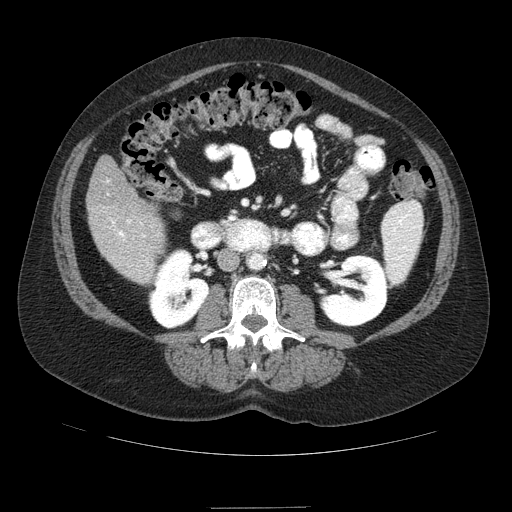
Contrast-enhanced abdominal CT (liver protocol), one axial slice; position 23 of 89 along the scan axis; reconstruction kernel STANDARD; 120 kVp; soft-tissue window (W 400 / L 40 HU); 2.5 mm slice thickness; 512 × 512 image matrix, field of view 400 × 400 mm. Case-level facts recorded for this patient, not image findings: diagnosis: hepatocellular carcinoma (patient treated with transarterial chemoembolisation; whether this scan precedes or follows treatment is not stated here); TNM stage (as recorded): Stage-IIIB; Child-Pugh class: A; tumour nodularity: multinodular.
Outlined on this slice (semi-automatic segmentation, software-assisted and operator-edited):
- liver parenchyma outside the tumour (the mass and vessels are separate outlines, so this box may not span the whole liver): bounding box (x1, y1, x2, y2) in pixels: (87, 156, 164, 282)
- liver vessels: (112, 219, 145, 237)